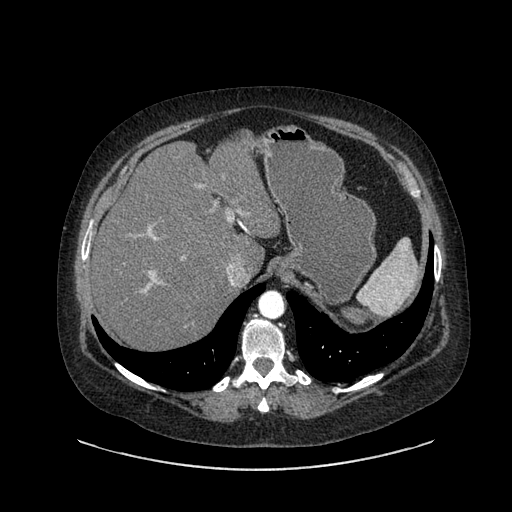
Contrast-enhanced abdominal CT, one axial slice. Position 645 of 769 along the scan axis. Reconstruction kernel SOFT. 120 kVp. Soft-tissue window (W 400 / L 40 HU). 0.62 mm slice thickness. 512 × 512 image matrix. Female patient, age 61 years. From the clinical record (not read from this slice): diagnosis: adrenocortical carcinoma; tumour side: left adrenal; tumour size at pathology: 13 cm; Ki-67 index: 79 %; stage (as recorded): 2.
Annotated regions visible in this slice (semi-automatically segmented with operator editing):
- mass: bounding box [x1, y1, x2, y2] px = [336, 305, 368, 332]